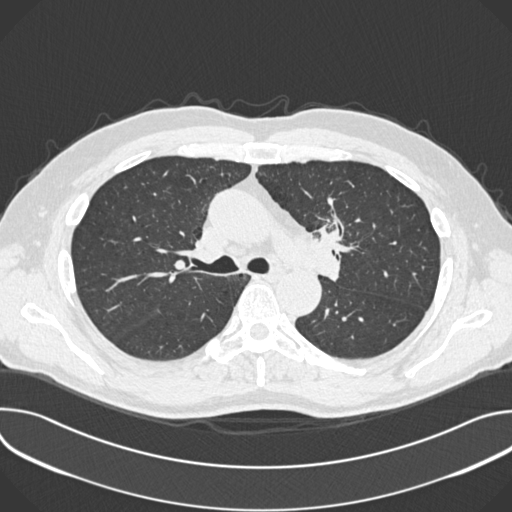
Low-dose screening chest CT, one axial slice; slice 245 of 361 in the series (ordered by position); 120 kVp; lung window (W 1500 / L -600 HU); 1 mm slice thickness; 512 × 512 image matrix.
Structures marked on this image (expert manual segmentation):
- lesion 1 (tumor, upper lobe of left lung): box from (x=319, y=220) to (x=344, y=245) px